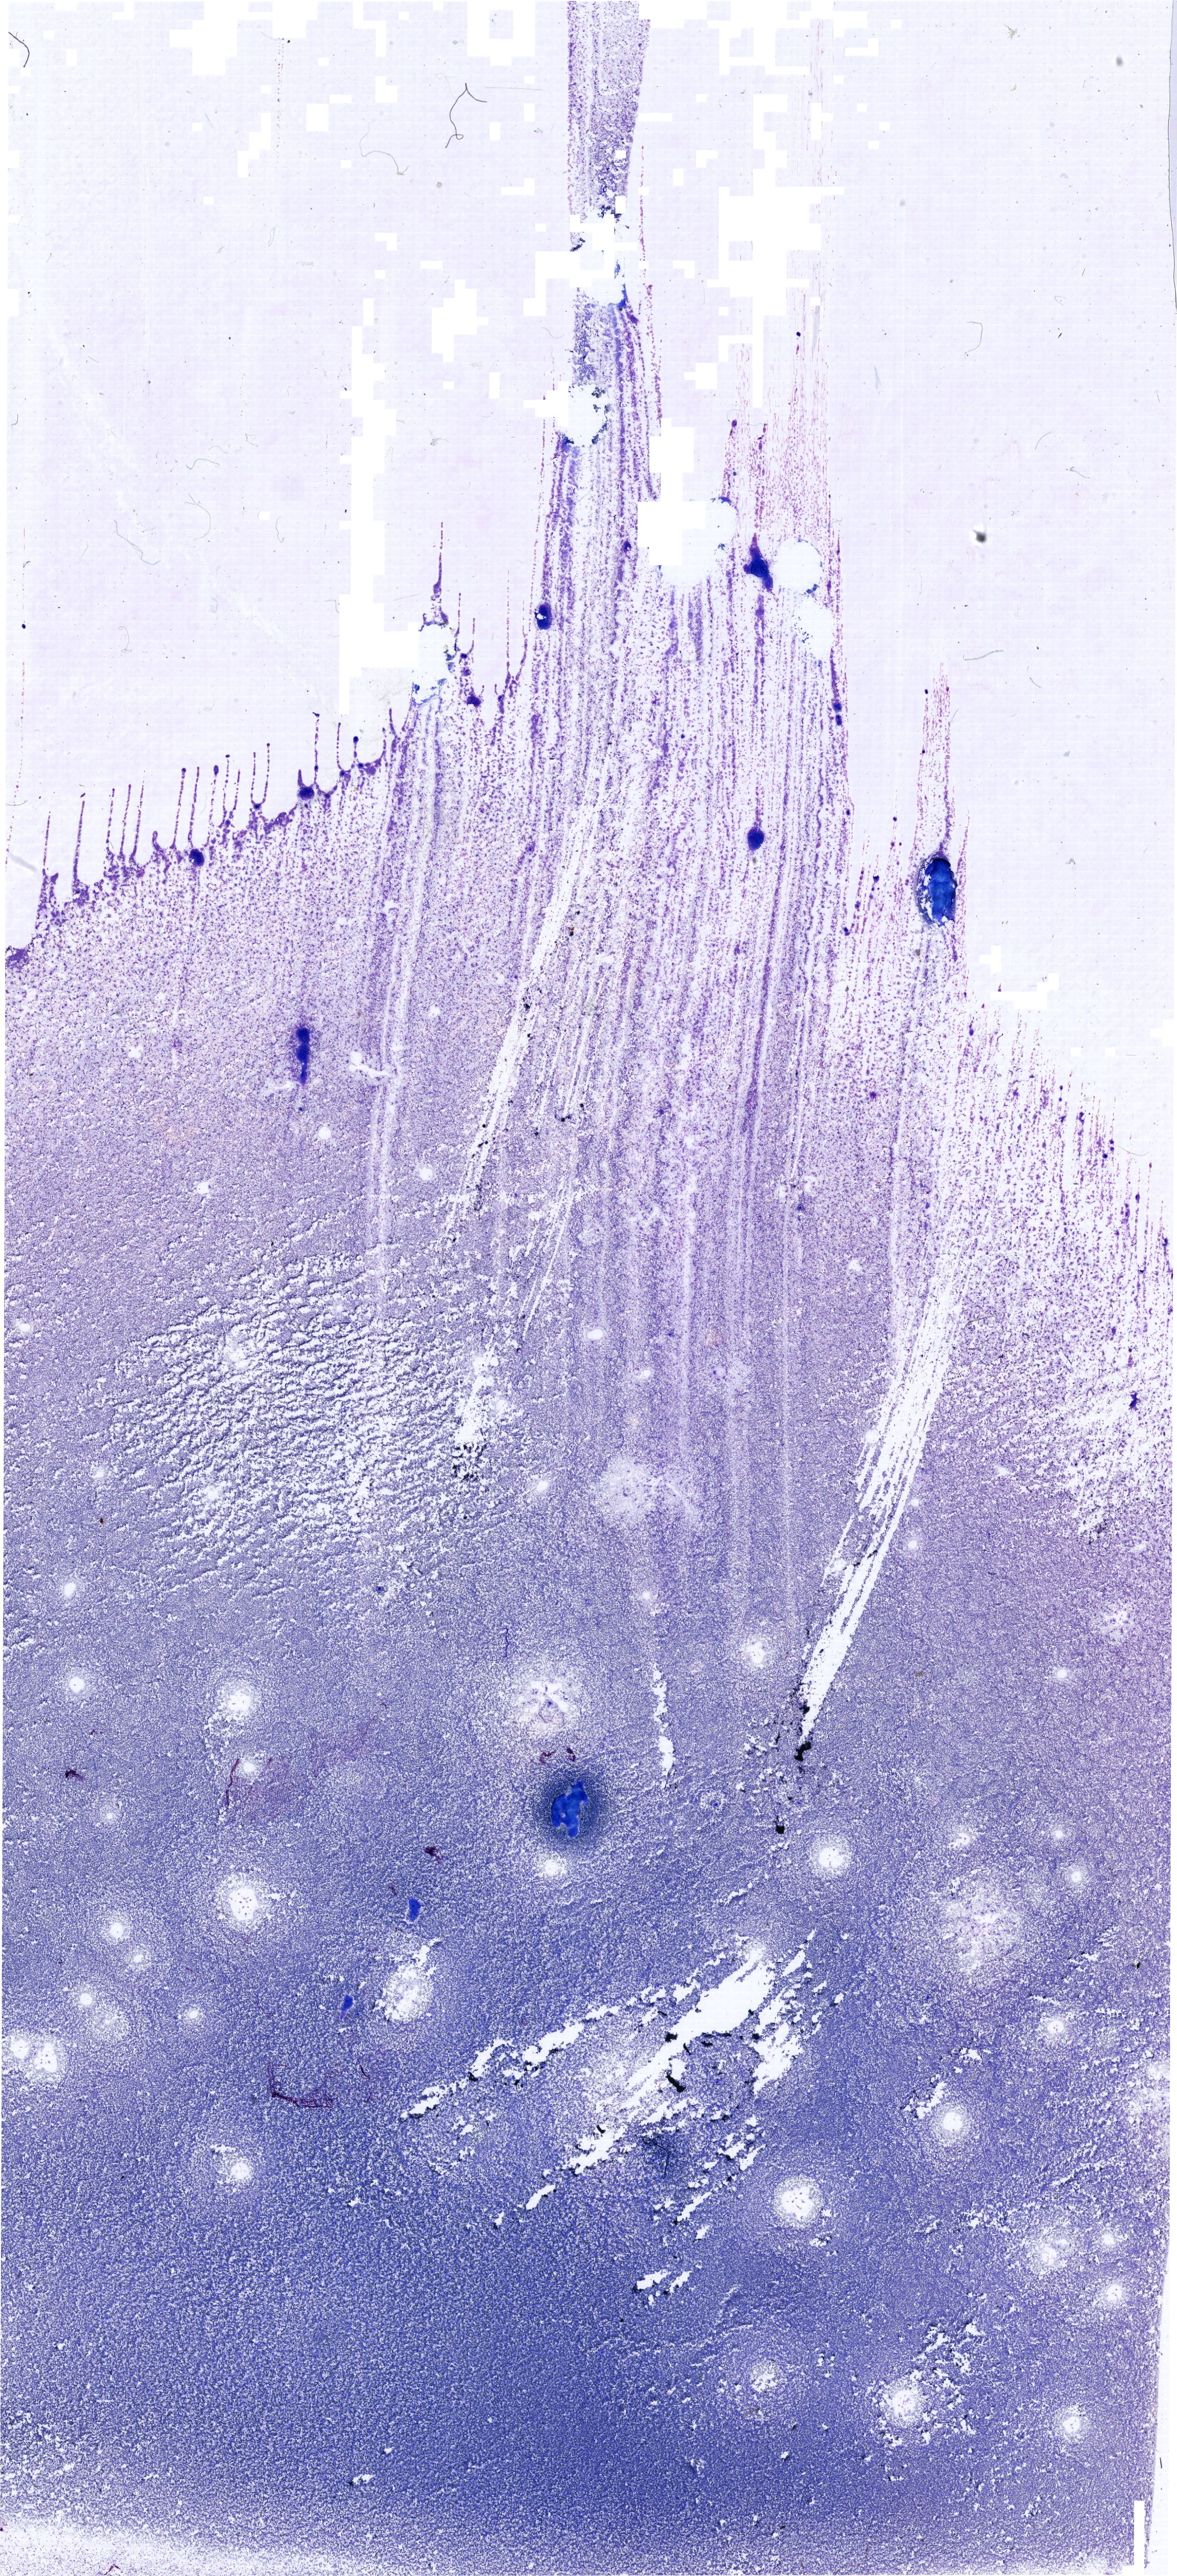
Whole-slide image of a May-Grünwald-Giemsa (MGG)-stained bone marrow aspirate smear — shown as a low-resolution overview of the whole scanned area (about 19.9 x 43.6 mm). Female patient.
Diagnosis: Mixed Phenotype Acute Leukemia, B/Myeloid.